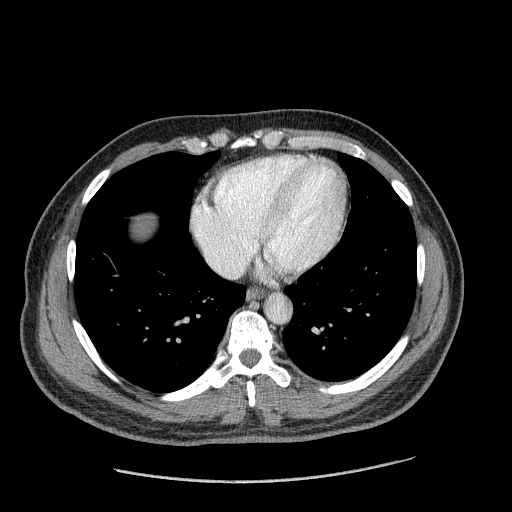
Contrast-enhanced abdominal CT (liver protocol), one axial slice. Slice 177 of 182 in the series (ordered by position). Reconstruction kernel STANDARD. Soft-tissue window (W 400 / L 40 HU). 2.5 mm slice thickness. 512 × 512 image matrix, field of view 400 × 400 mm. Case-level facts recorded for this patient, not image findings: diagnosis: hepatocellular carcinoma (patient treated with transarterial chemoembolisation; whether this scan precedes or follows treatment is not stated here); TNM stage (as recorded): Stage-I; Child-Pugh class: A; tumour differentiation: well differentiated; tumour nodularity: uninodular.
Structures marked on this image (semi-automatic segmentation, software-assisted and operator-edited):
- abdominal aorta: bounding box [x1, y1, x2, y2] px = [265, 296, 291, 323]
- liver parenchyma outside the tumour (the mass and vessels are separate outlines, so this box may not span the whole liver): [134, 214, 154, 236]